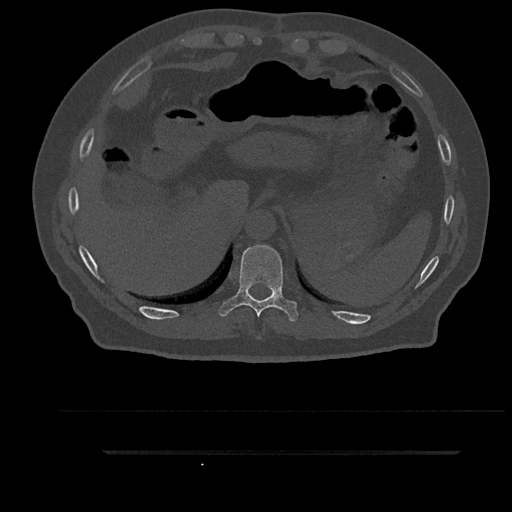
CT including the spine, one axial slice; position 368 of 797 along the scan axis; reconstruction kernel Br40s/3; 120 kVp; bone window (W 1800 / L 400 HU); 0.5 mm slice thickness; 512 × 512 image matrix. Patient: male, 63 years. From the clinical record (not read from this slice): primary cancer: renal; vertebrae with lytic lesions (as recorded): T8.
Structures marked on this image (semi-automatically segmented with operator editing):
- T10 vertebra: bounding box [x1, y1, x2, y2] px = [218, 244, 298, 321]